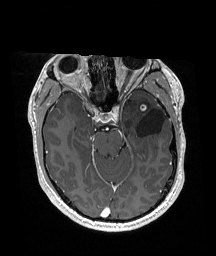
Brain MRI from a brain-tumour surgery series, one axial slice. Position 113 of 192 along the scan axis. T1-weighted post-contrast. 1 mm slice thickness. 216 × 256 image matrix, field of view 211 × 250 mm. Case-level facts recorded for this patient, not image findings: histopathology: Glioneuronal tumor; WHO grade: 2; tumour location: Left Superior Temporal Gyrus.
Outlined on this slice (expert manual segmentation):
- previous resection cavity: bounding box <136,108,166,137> (left, top, right, bottom; pixels)
- tumour: <140,104,148,112>